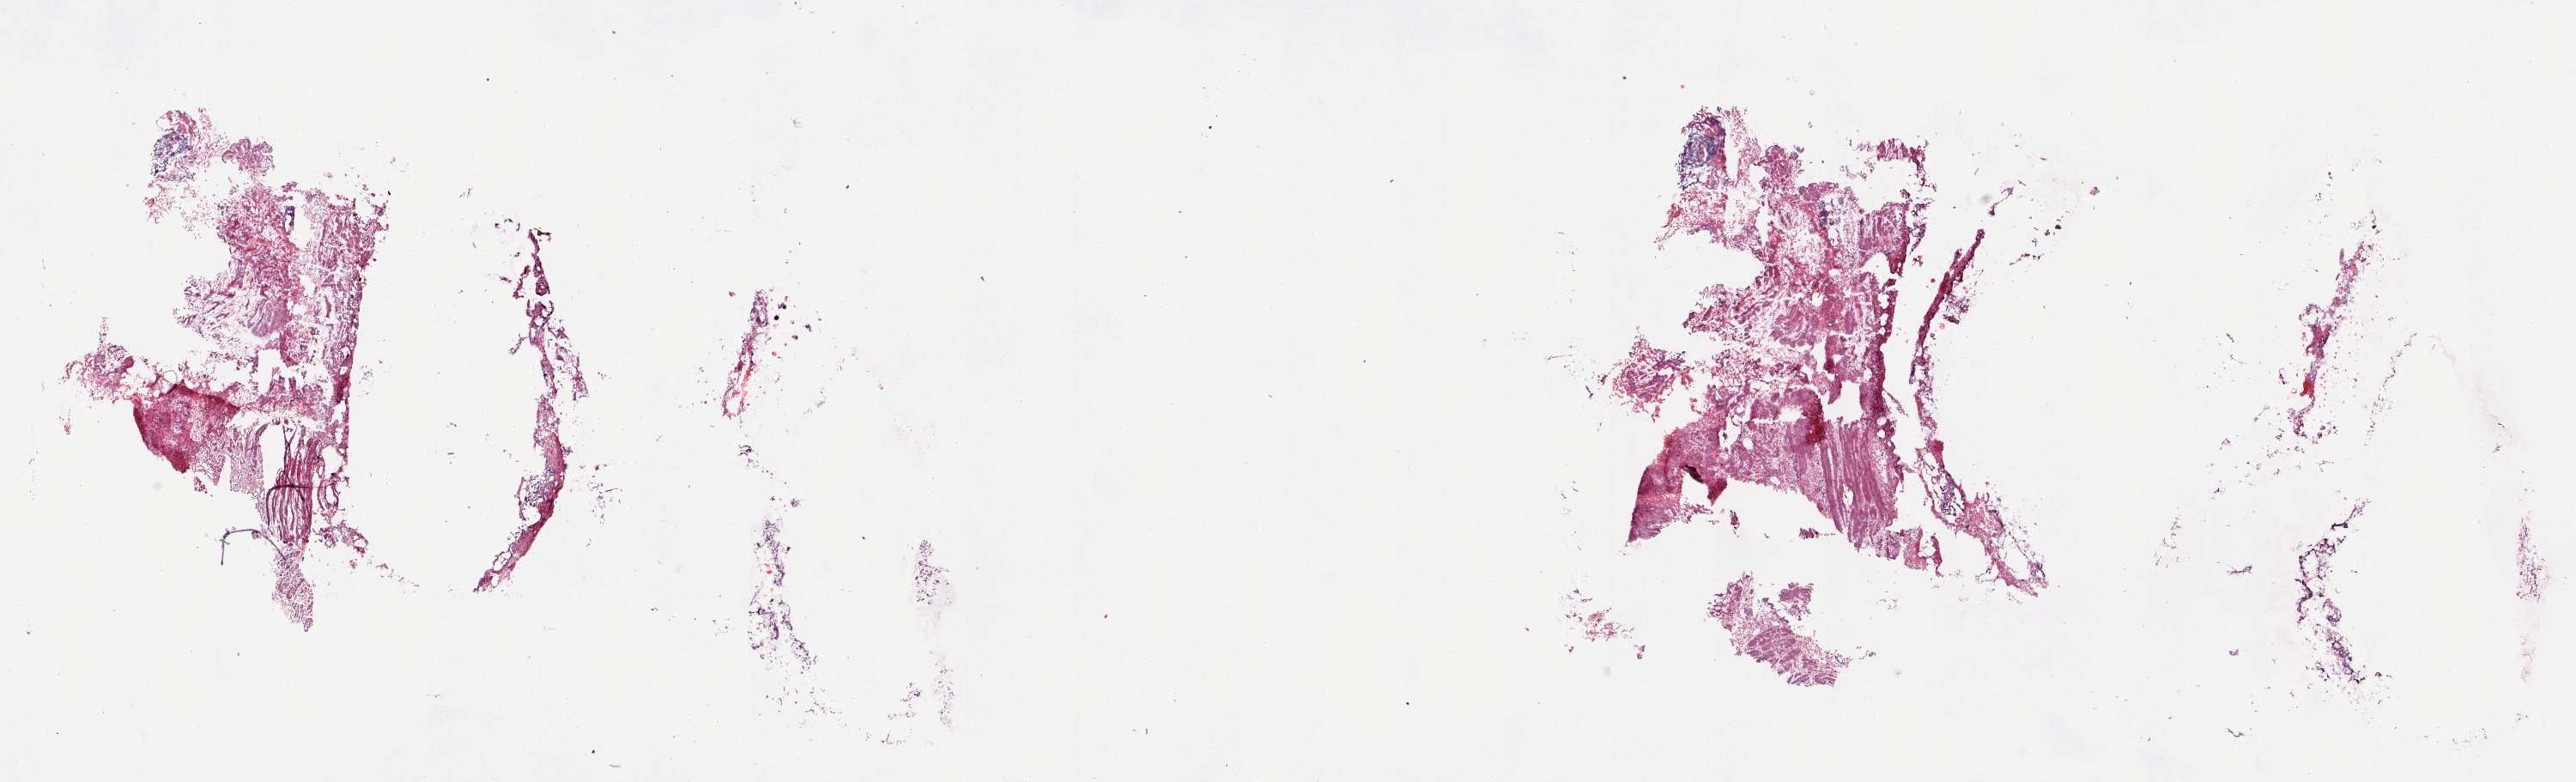
Whole-slide histology image, H&E-stained — whole scanned area (about 23.8 x 7.2 mm) shown as a low-resolution overview, frozen section, esophagus, solid tissue normal (non-tumour tissue) sample. Male patient; age at initial diagnosis 65 years. Slide review estimates, as recorded: tumour cells 0%, tumour nuclei 0%, normal cells 100%, stromal cells 0%, necrosis 0%. Inflammatory infiltration, as recorded: lymphocyte infiltration 1%, monocyte infiltration 0%, neutrophil infiltration 0%.
• this section: solid tissue normal sample (biorepository sample class)
• patient diagnosis: Adenocarcinoma, NOS (lower third of esophagus)